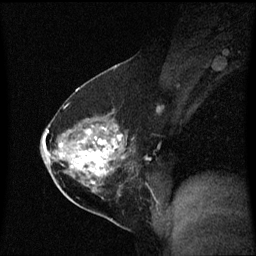
Breast MRI (dynamic contrast-enhanced), one sagittal slice; slice 33 of 60 in the series (ordered by position); dynamic contrast-enhanced series, image 2 of 3 at this slice position (ordered by acquisition); 1.5 T; TE 4.2 ms, TR 8.4 ms; 2 mm slice thickness; 256 × 256 image matrix. Patient: female, 54 years. From the clinical record (not read from this slice): setting: breast cancer imaged before/during neoadjuvant chemotherapy; receptor status: HER2-positive.
Annotated regions visible in this slice (semi-automatically segmented with operator editing):
- analysis volume of interest (the breast-tissue region the enhancement analysis was run in; not a lesion): box from (x=59, y=115) to (x=141, y=199) px
- tumour enhancement mask (voxels above the 70 % enhancement threshold inside the analysis volume of interest): (x=59, y=128)–(x=124, y=185)